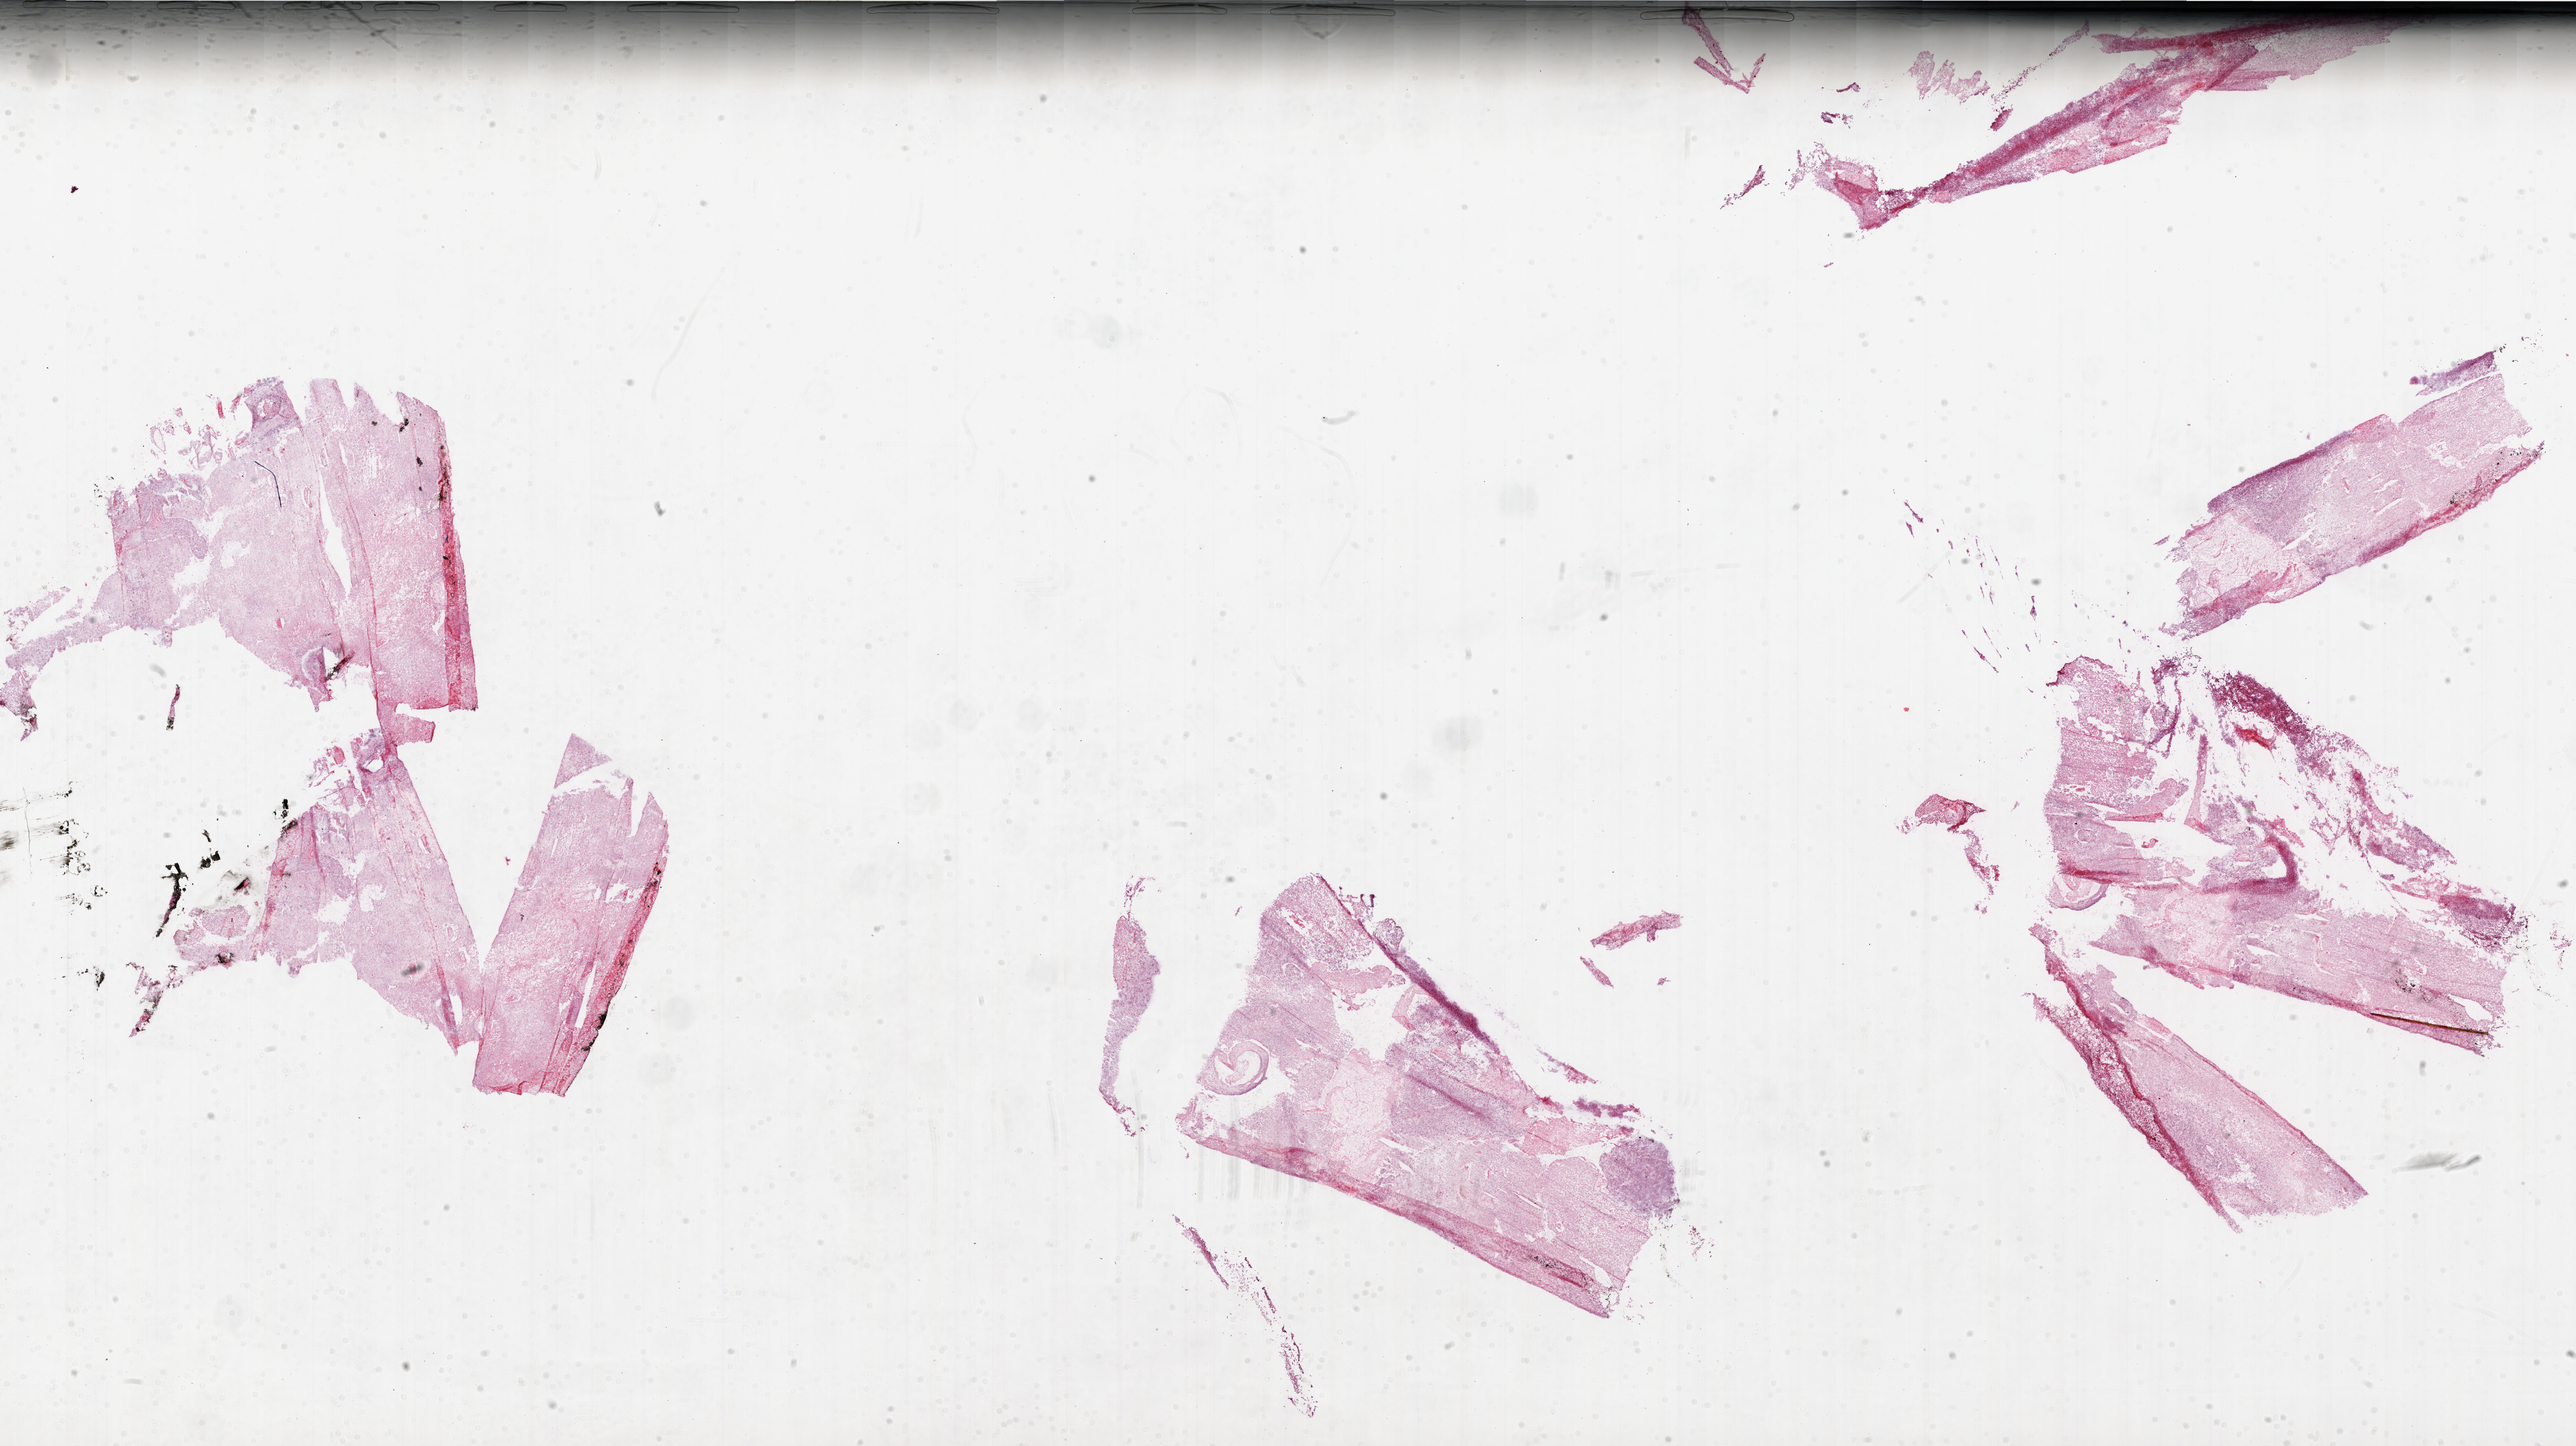
Whole-slide histology image, H&E-stained — whole scanned area (about 39.0 x 21.9 mm, slide scanned at 20x) shown as a low-resolution overview, frozen section, primary tumour sample from the brain. Male, age 86 years at initial diagnosis. Composition of this section per pathologist review: tumour cells 25%, tumour nuclei 100%, normal cells 0%, stromal cells 0%, necrosis 75%. Infiltration values recorded for this section: lymphocyte infiltration 0%, monocyte infiltration 0%, neutrophil infiltration 0%.
• pathologic diagnosis: Glioblastoma